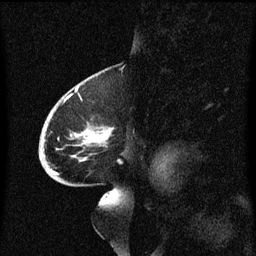
Breast MRI (dynamic contrast-enhanced), one sagittal slice; slice 37 of 60 in the series (ordered by position); dynamic contrast-enhanced series, image 2 of 3 at this slice position (ordered by acquisition); 1.5 T; TE 4.2 ms, TR 8.4 ms; 2 mm slice thickness; 256 × 256 image matrix, field of view 200 × 200 mm. Patient: female, 68 years. From the clinical record (not read from this slice): setting: breast cancer imaged before/during neoadjuvant chemotherapy; receptor status: triple-negative.
Annotated regions visible in this slice (semi-automatic segmentation, software-assisted and operator-edited):
- analysis volume of interest (the breast-tissue region the enhancement analysis was run in; not a lesion): bounding box (x1, y1, x2, y2) in pixels: (40, 94, 123, 173)
- tumour enhancement mask (voxels above the 70 % enhancement threshold inside the analysis volume of interest): (42, 130, 112, 173)